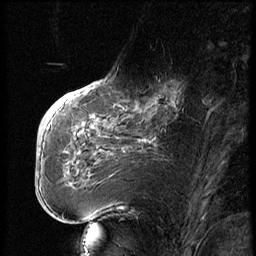
Breast MRI (dynamic contrast-enhanced), one sagittal slice; position 25 of 74 along the scan axis; dynamic contrast-enhanced series, image 2 of 3 at this slice position (ordered by acquisition); 1.5 T; TE 4.2 ms, TR 9 ms; 256 × 256 image matrix. Patient: female, 56 years. Case-level facts recorded for this patient, not image findings: setting: breast cancer imaged before/during neoadjuvant chemotherapy.
Structures marked on this image (semi-automatic segmentation, software-assisted and operator-edited):
- analysis volume of interest (the breast-tissue region the enhancement analysis was run in; not a lesion): bounding box [x1, y1, x2, y2] px = [123, 71, 195, 131]
- tumour enhancement mask (voxels above the 140 % enhancement threshold inside the analysis volume of interest): [133, 82, 181, 113]